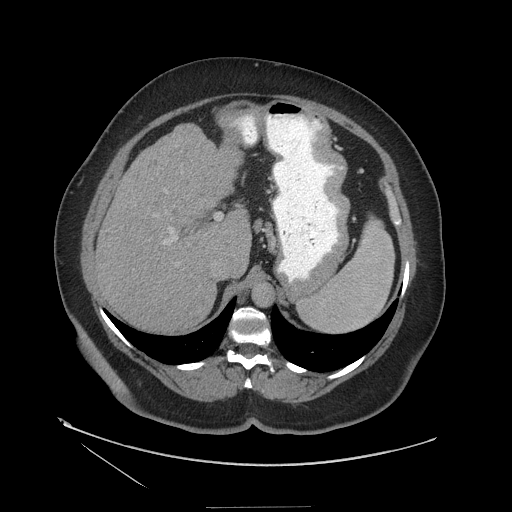
Contrast-enhanced abdominal CT (liver protocol), one axial slice; position 81 of 127 along the scan axis; reconstruction kernel STANDARD; 140 kVp; soft-tissue window (W 400 / L 40 HU); 2.5 mm slice thickness; 512 × 512 image matrix, field of view 480 × 480 mm. From the clinical record (not read from this slice): diagnosis: hepatocellular carcinoma (patient treated with transarterial chemoembolisation; whether this scan precedes or follows treatment is not stated here); TNM stage (as recorded): Stage-II; Child-Pugh class: A; tumour differentiation: well differentiated; tumour nodularity: multinodular.
Annotated regions visible in this slice (semi-automatically segmented with operator editing):
- liver parenchyma outside the tumour (the mass and vessels are separate outlines, so this box may not span the whole liver): bounding box (x1, y1, x2, y2) in pixels: (96, 114, 256, 330)
- liver vessels: (171, 116, 256, 239)